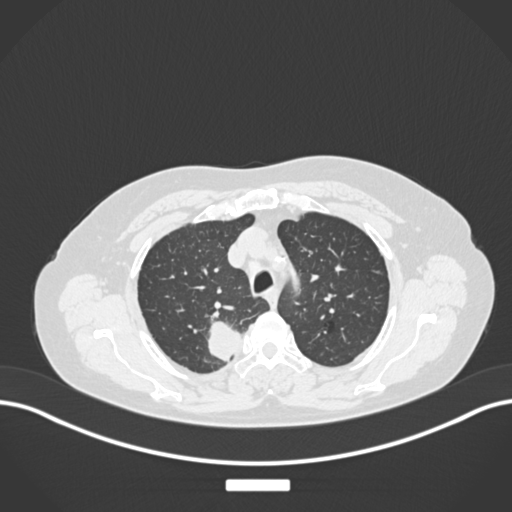
Chest CT, one axial slice. Slice 203 of 237 in the series (ordered by position). Reconstruction kernel B30f. 120 kVp. Lung window (W 1500 / L -600 HU). 1 mm slice thickness. 512 × 512 image matrix, field of view 400 × 400 mm. Patient: female, 62 years. Case-level facts recorded for this patient, not image findings: clinical TNM (as recorded): T1c N1 M0.
Structures marked on this image (rectangle marked by the reading radiologist):
- lung tumour (recorded histology: squamous cell carcinoma): bounding box (x1, y1, x2, y2) in pixels: (205, 317, 244, 365)